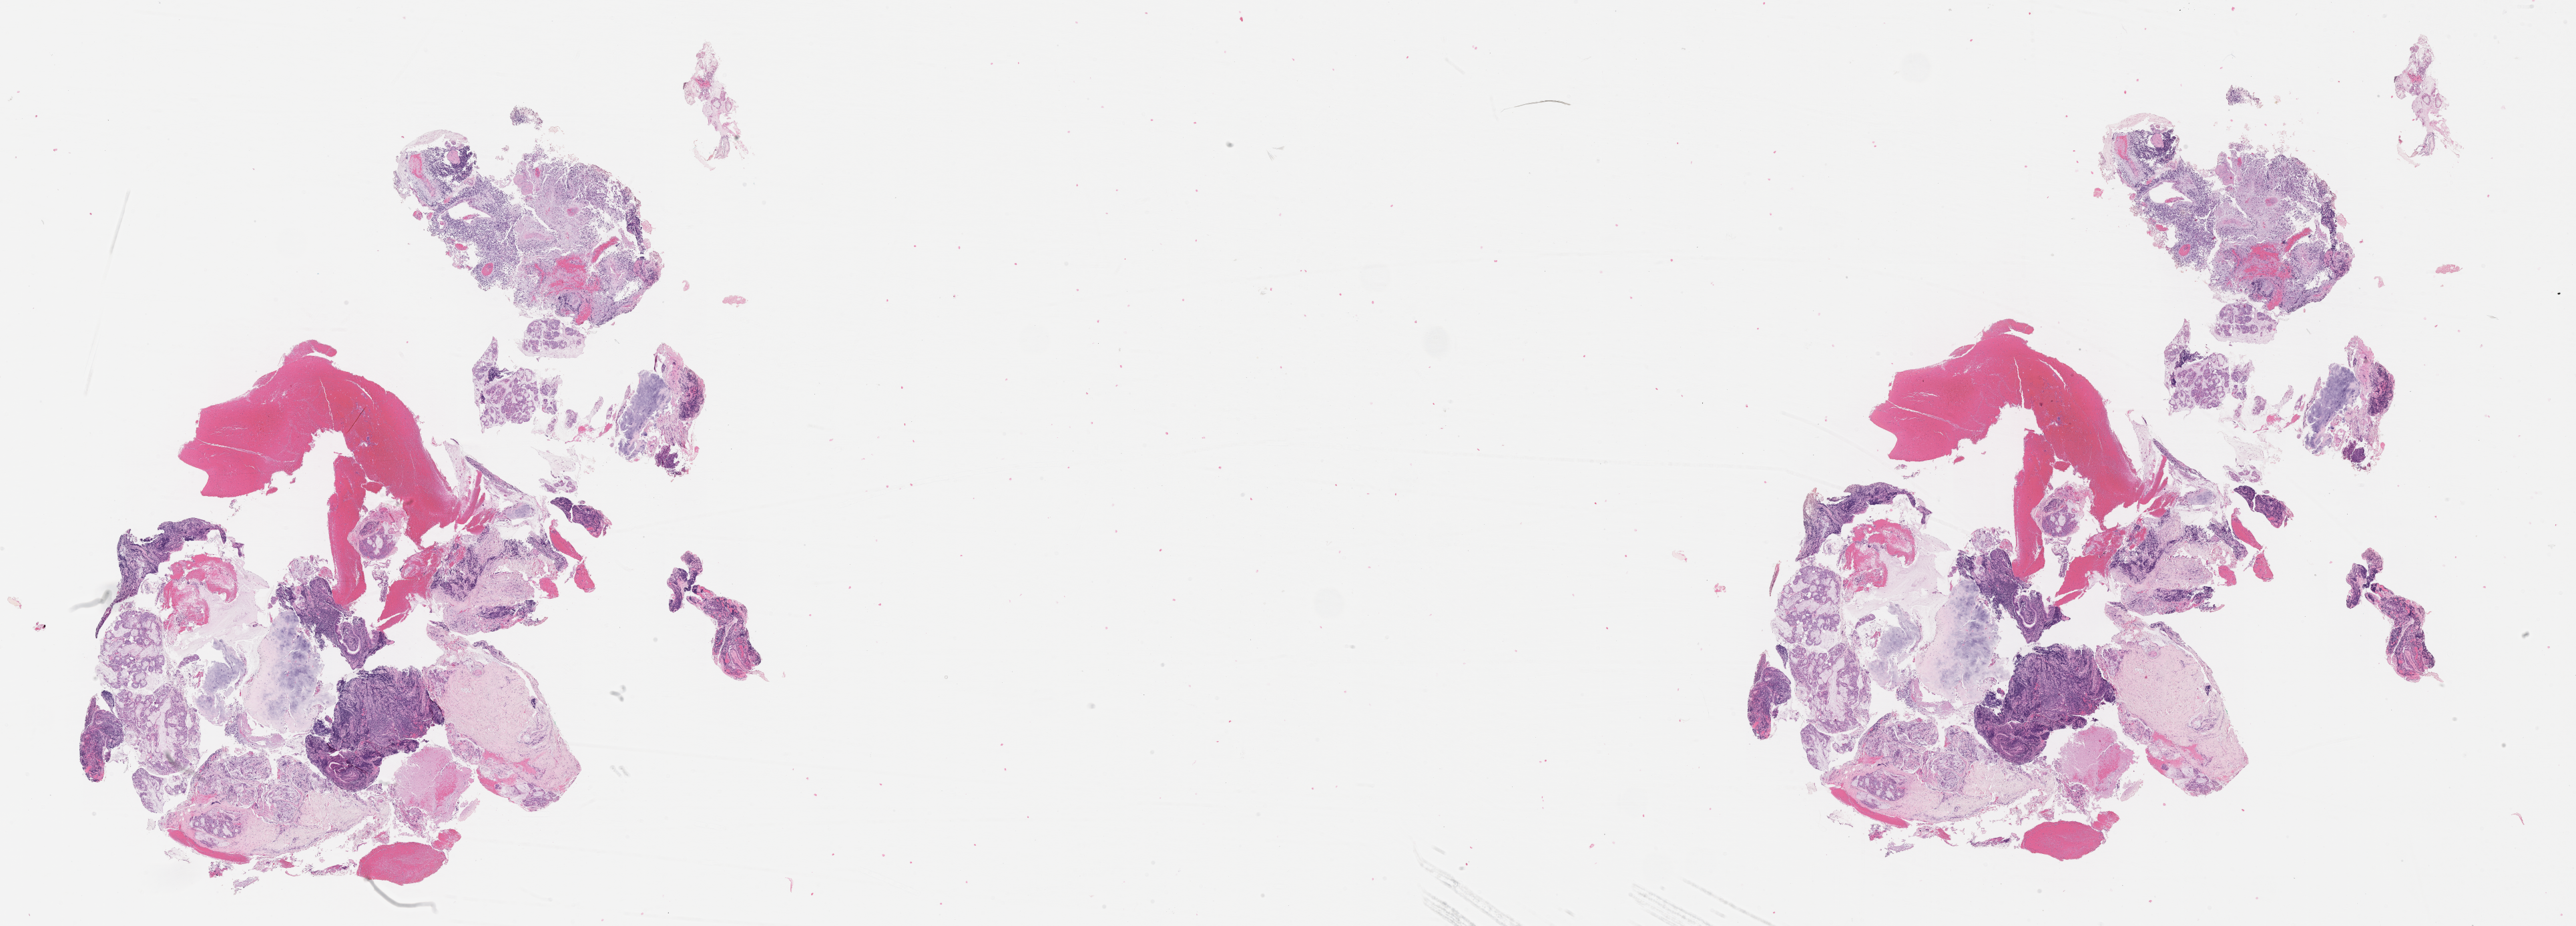
Whole-slide image, H&E stain of tumor tissue — a low-resolution overview of the entire scanned area, about 31.2 x 11.2 mm, formalin-fixed paraffin-embedded section, sample anatomic site: nasopharynx. Patient: male, age 9.6 years at diagnosis.
Diagnosis: rhabdomyosarcoma; histological classification: embryonal rhabdomyosarcoma.